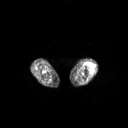
FDG PET of an extremity soft-tissue mass (from a PET/CT study), one axial slice. Slice 193 of 267 in the series (ordered by position). 3.27 mm slice thickness. 128 × 128 image matrix. Female patient, age 62 years. From the clinical record (not read from this slice): histological type: undifferentiated – high grade; grade: high; site of the primary tumour: left thigh.
Annotated regions visible in this slice (expert contour drawn on MRI and transferred to this co-registered scan by the dataset authors):
- gross tumour volume including surrounding oedema: bounding box [x1, y1, x2, y2] px = [85, 63, 95, 72]